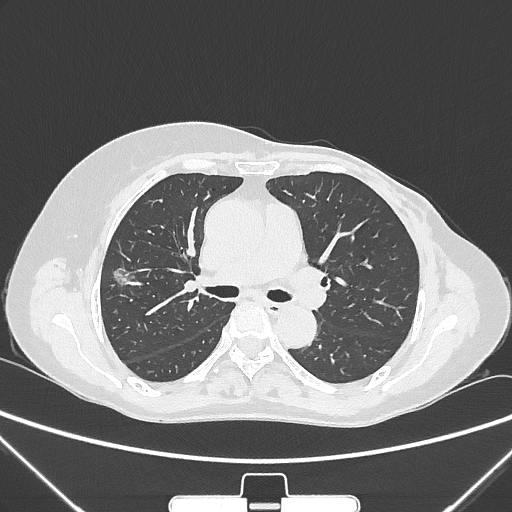
Chest CT, one axial slice; reconstruction kernel IMR1,SharpPlus; lung window (W 1500 / L -600 HU); 1 mm slice thickness; 512 × 512 image matrix. Patient: female, 64 years. Case-level facts recorded for this patient, not image findings: clinical TNM (as recorded): T1c N0 M0; histopathological grade: G1-2.
Annotated regions visible in this slice (rectangle marked by the reading radiologist):
- lung tumour (recorded histology: adenocarcinoma): bounding box [x1, y1, x2, y2] px = [105, 257, 134, 290]